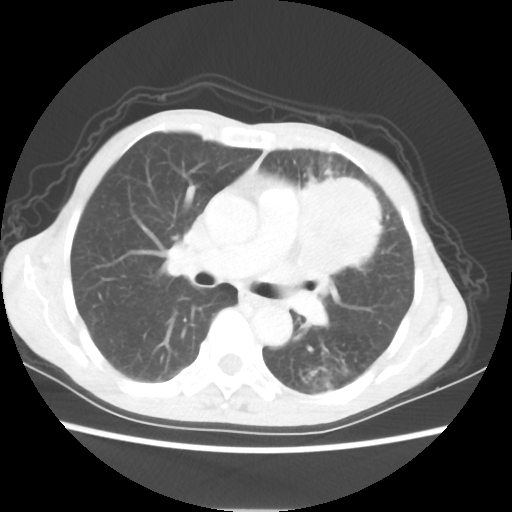
Chest CT, one axial slice. Reconstruction kernel STANDARD. Lung window (W 1500 / L -600 HU). 512 × 512 image matrix, field of view 331 × 331 mm. Patient: female, 60 years. Case-level facts recorded for this patient, not image findings: clinical TNM (as recorded): T4 N1 M0.
Structures marked on this image (rectangle marked by the reading radiologist):
- lung tumour (recorded histology: adenocarcinoma): box from (x=295, y=171) to (x=389, y=283) px